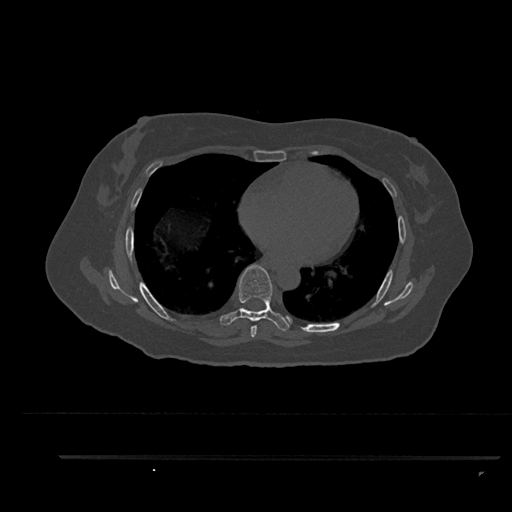
CT including the spine, one axial slice; slice 514 of 797 in the series (ordered by position); 120 kVp; bone window (W 1800 / L 400 HU); 0.5 mm slice thickness; 512 × 512 image matrix, field of view 408 × 408 mm. Female patient, age 44 years. Case-level facts recorded for this patient, not image findings: primary cancer: renal; vertebrae with lytic lesions (as recorded): L1.
Outlined on this slice (semi-automatic segmentation, software-assisted and operator-edited):
- T6 vertebra: box from (x=251, y=325) to (x=257, y=337) px
- T7 vertebra: (x=220, y=264)–(x=291, y=331)